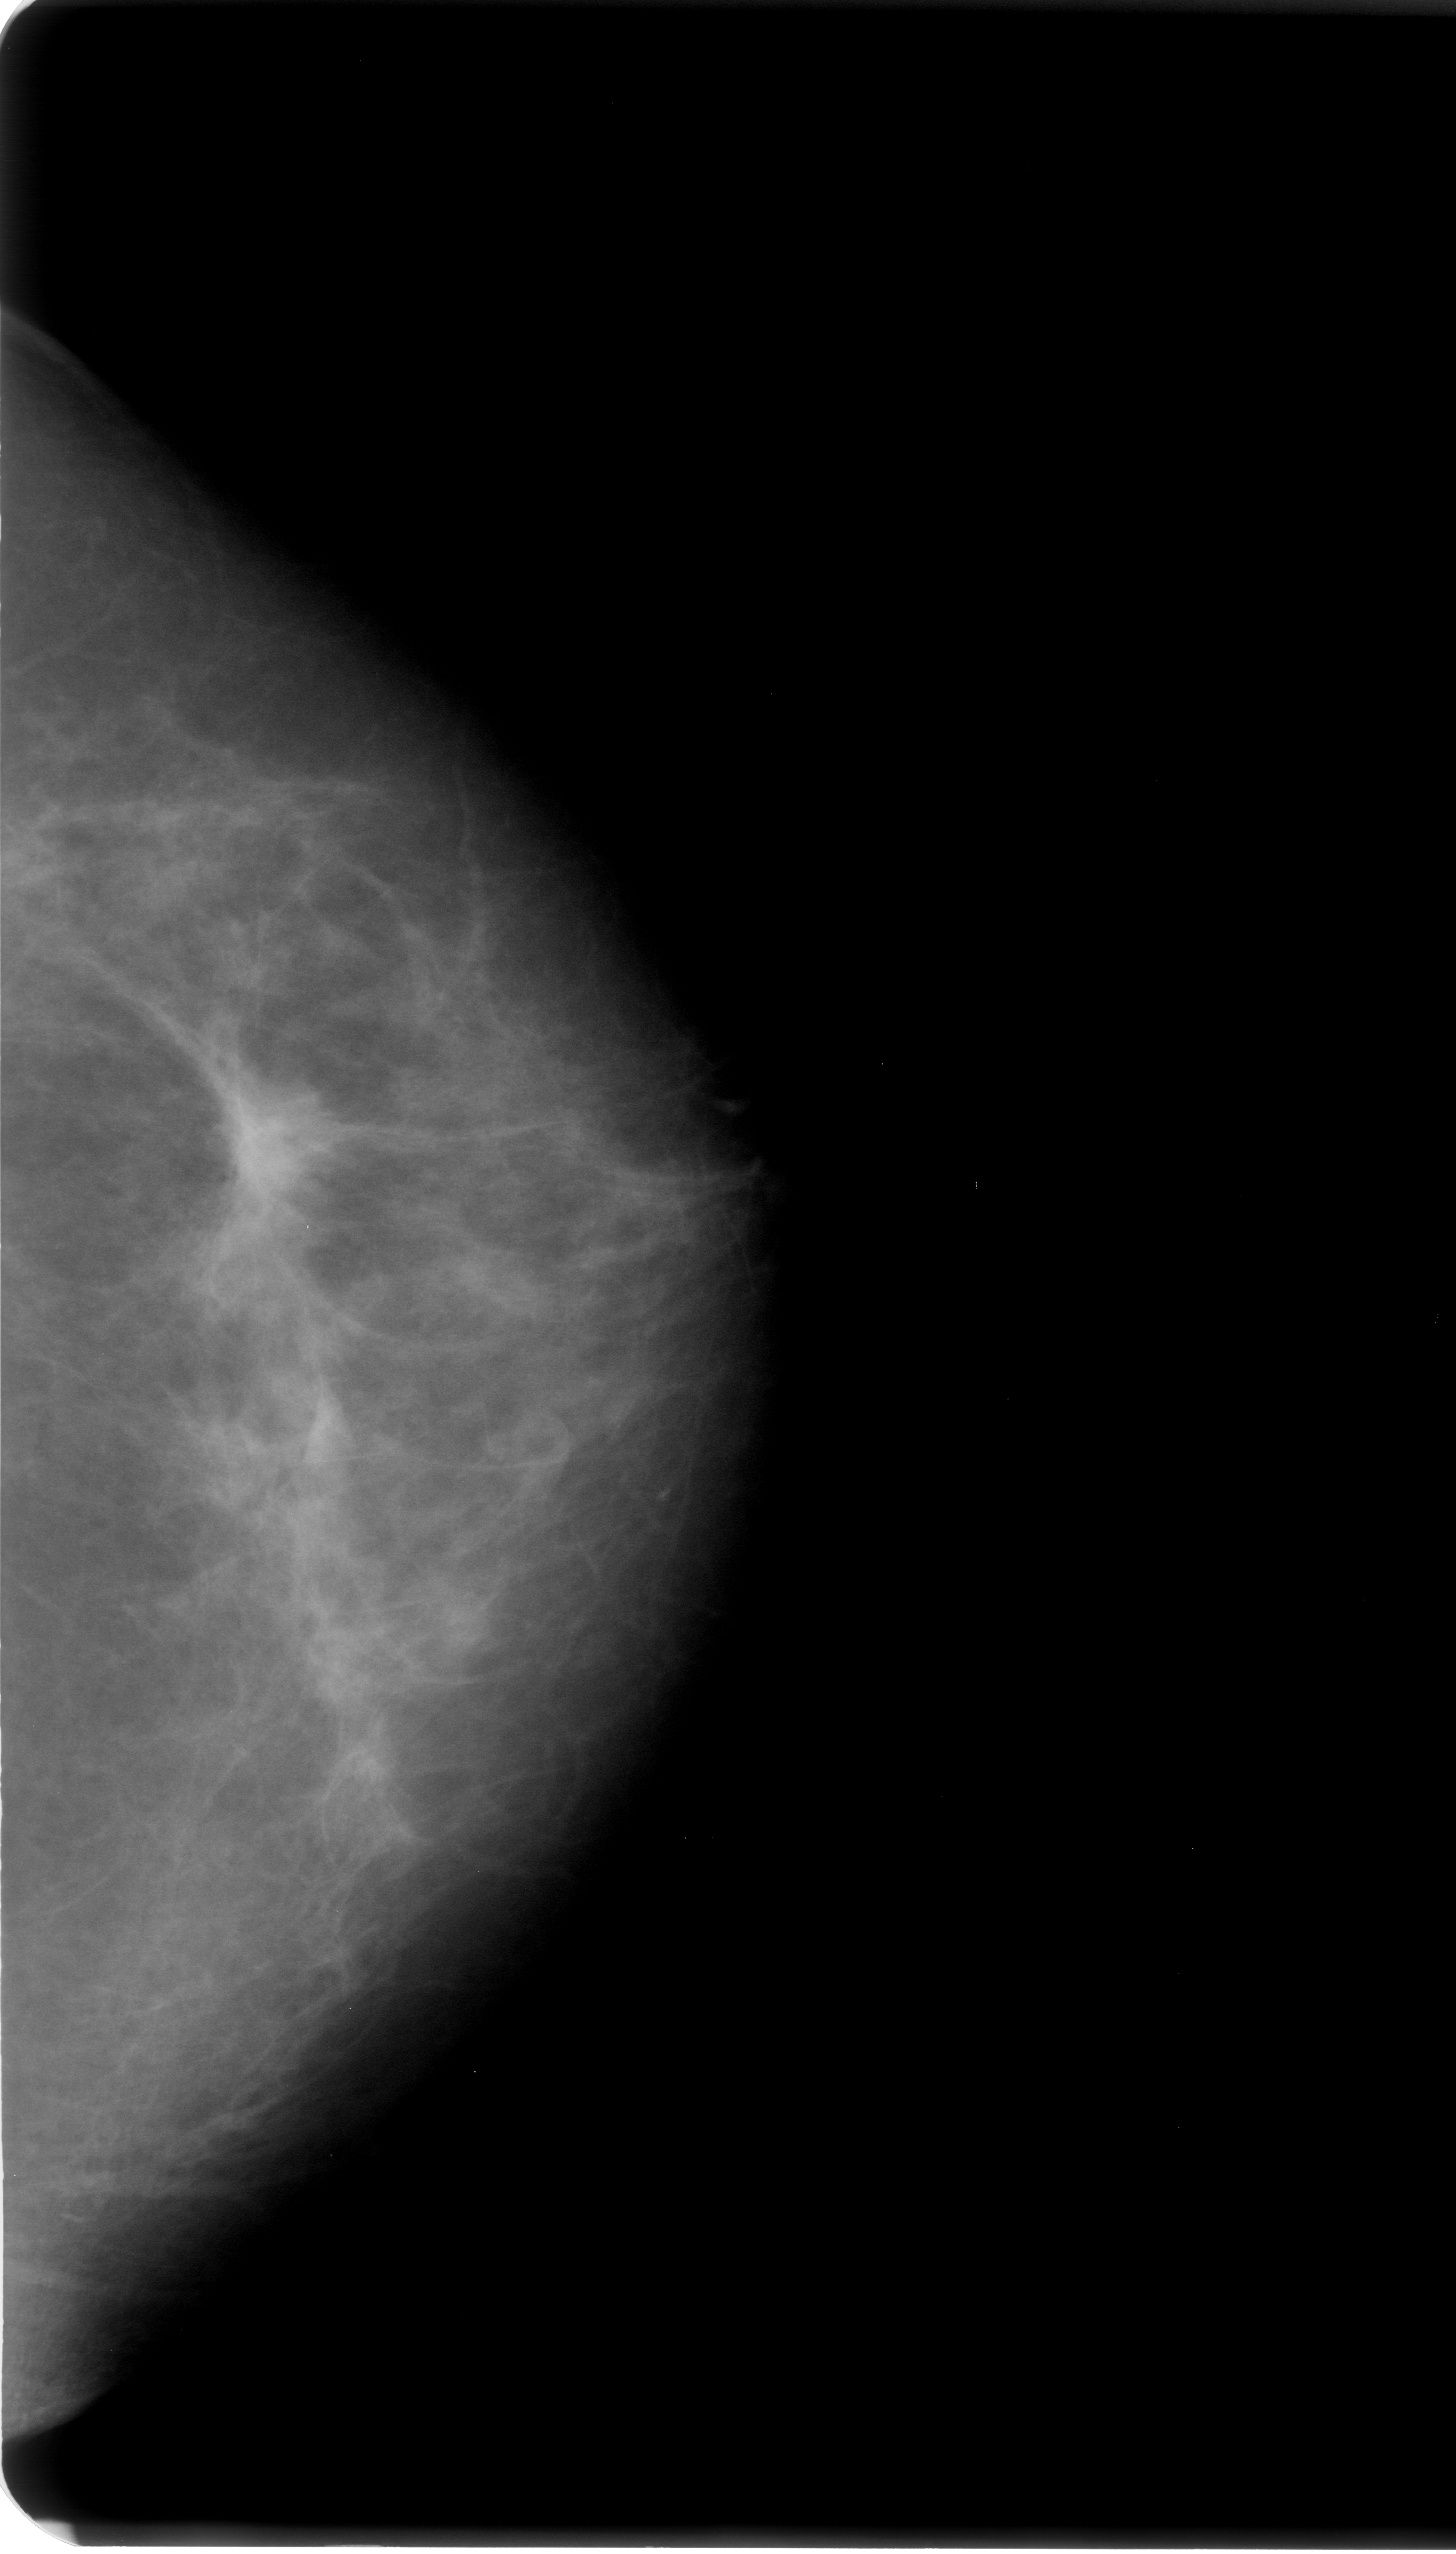
Mammogram (digitized film); left breast; CC view; BI-RADS breast density category 3 (scale 1–4).
Marked findings (only marked abnormalities are described; nothing is implied about the rest of the image): mass, shape irregular / architectural distortion, margins spiculated; BI-RADS assessment category 4; subtlety rating 4 on a 1 (subtle) to 5 (obvious) scale; pathology (as recorded): malignant.